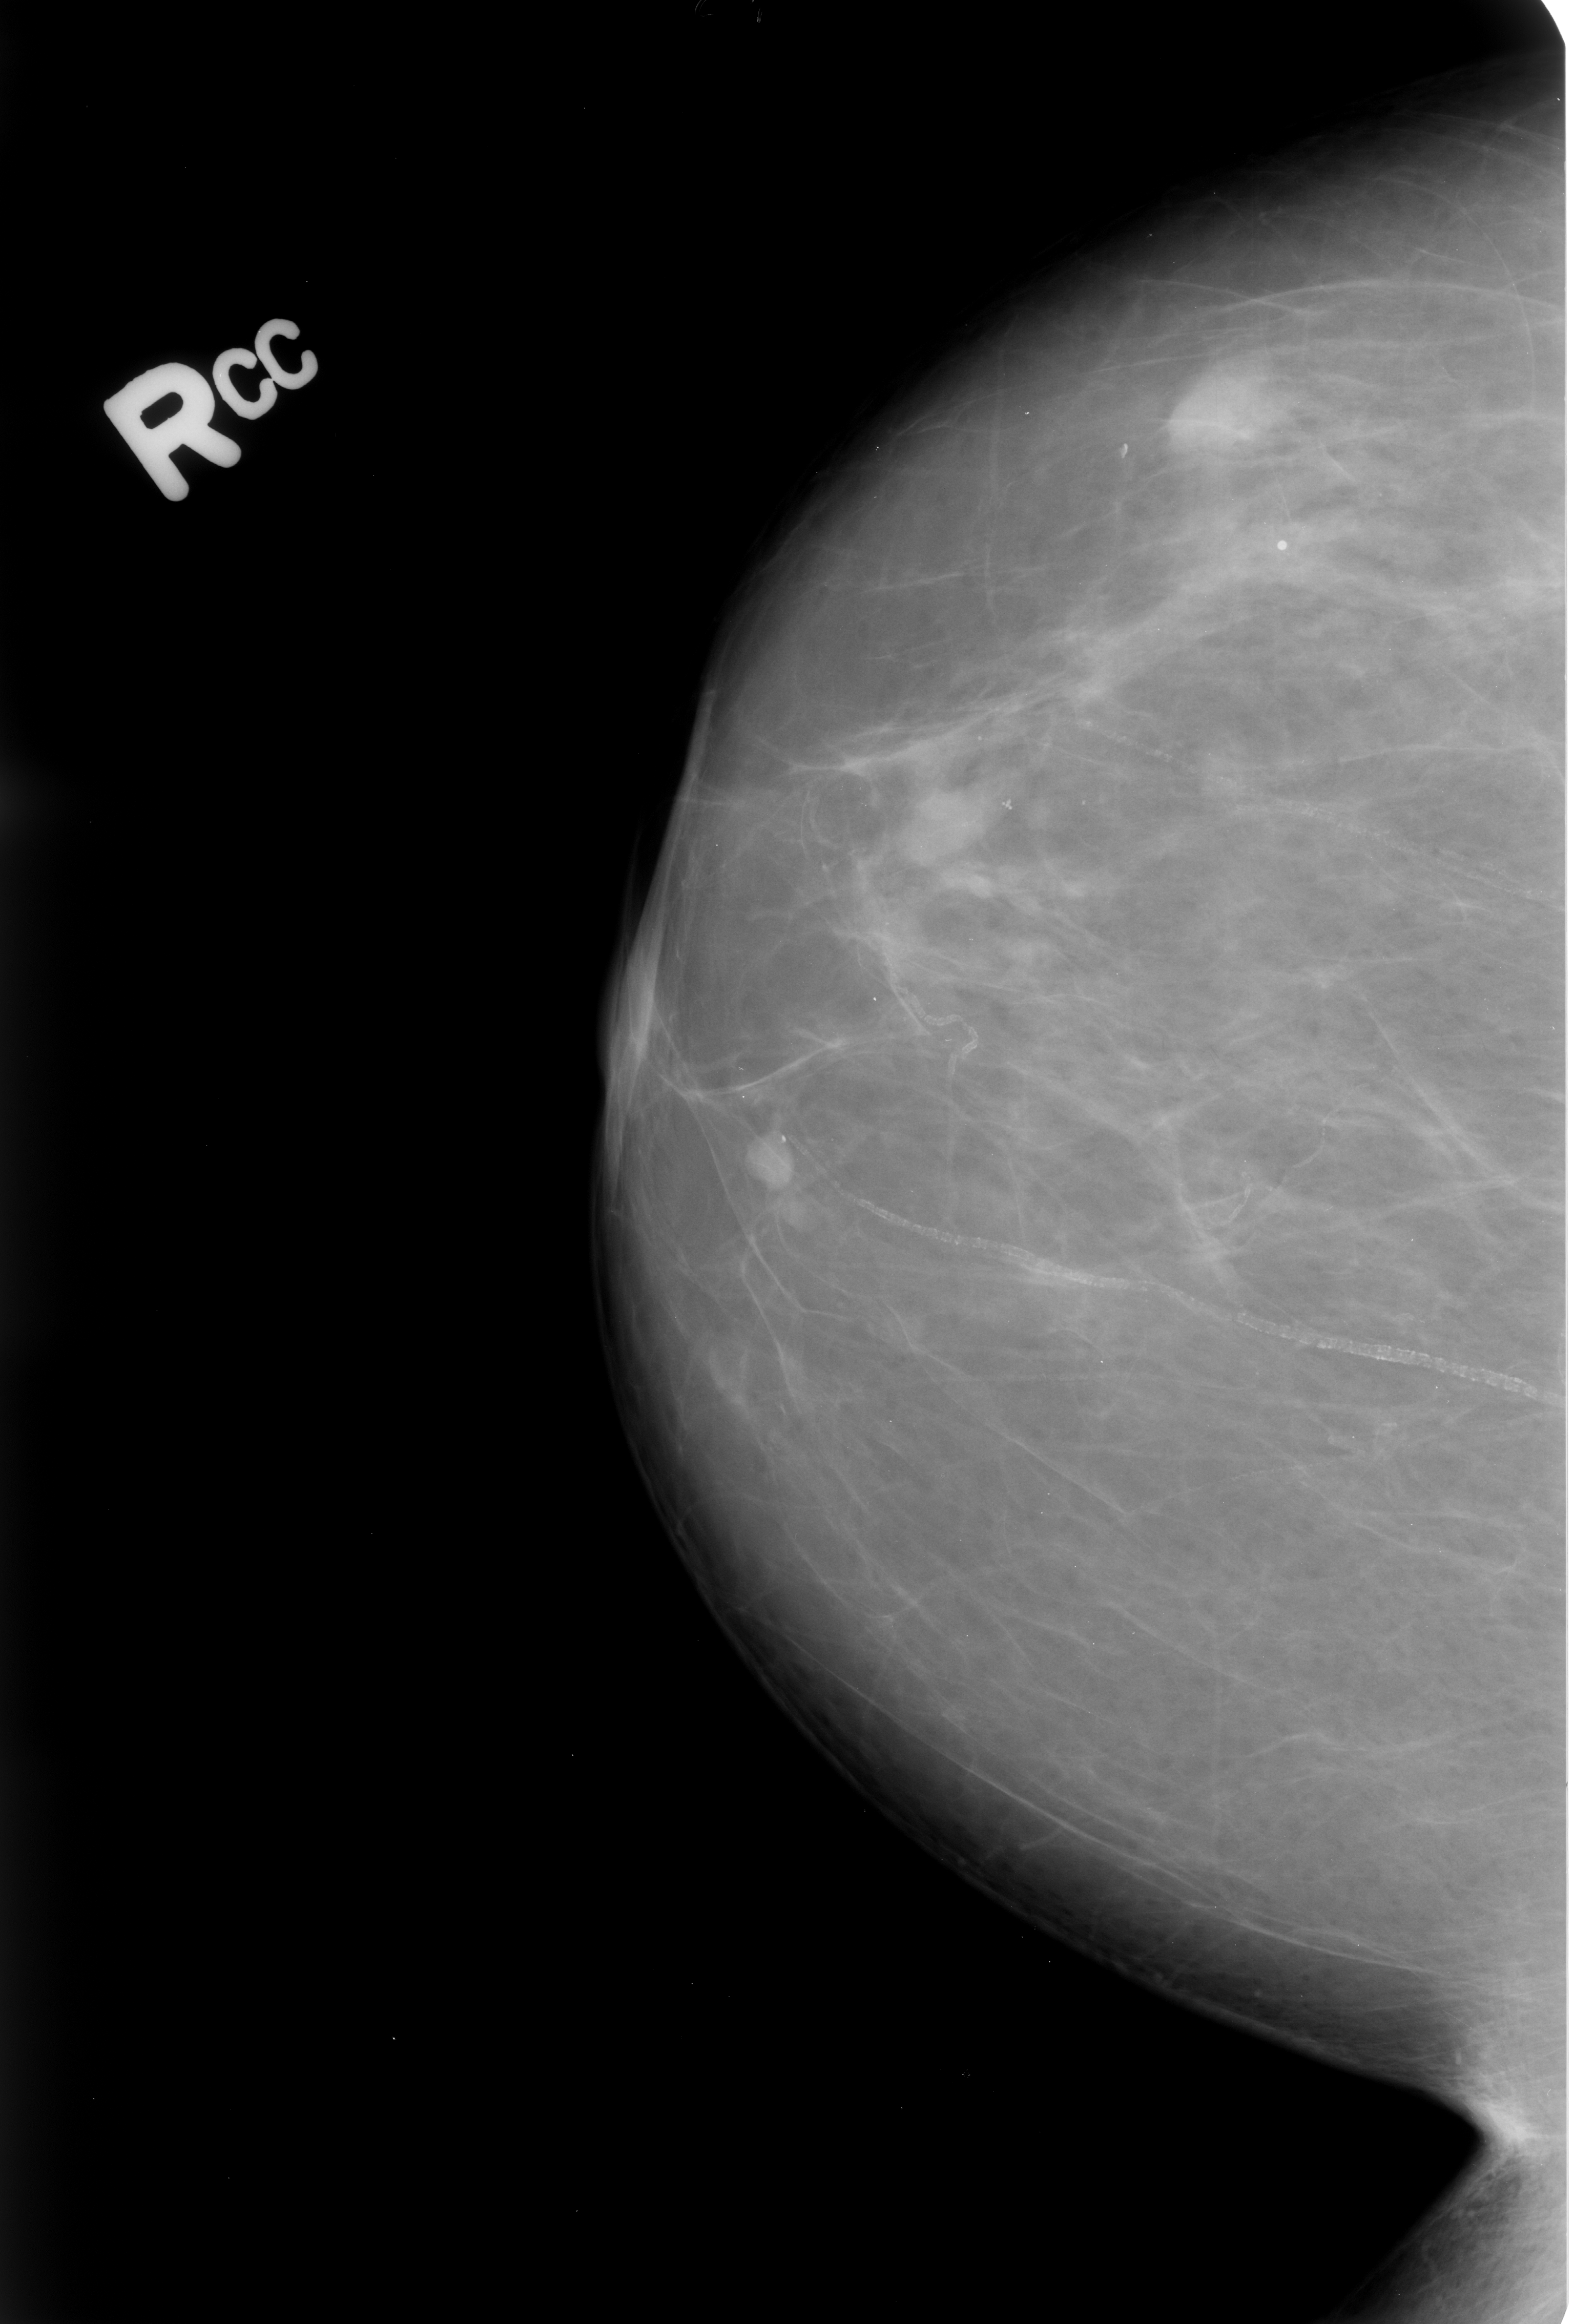
Mammogram (digitized film); right breast; craniocaudal (CC) view; breast composition: scattered fibroglandular densities (BI-RADS density category 2 of 4); 1574 × 2324 image matrix.
Expert-marked regions of interest on this film, with their recorded descriptors:
- Finding 1 of 2: calcifications, morphology vascular; BI-RADS assessment category 2; benign; no additional work-up was recommended (outcome (as recorded, no biopsy): benign without callback): bounding box <827,1184,1559,1423> (left, top, right, bottom; pixels)
- Finding 2 of 2: calcifications, morphology round and regular; BI-RADS assessment category 2; outcome (as recorded, no biopsy): benign without callback (not worked up further): <1246,512,1321,579>